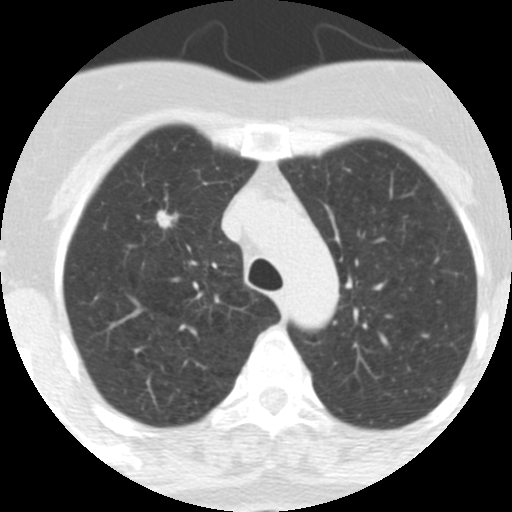
Axial slice from a low-dose chest CT screening exam; baseline annual screen; lung window (W 1500 / L -600 HU); 2.5 mm slice thickness; 120 kVp; slice 74 of 313 in the series. Female participant, aged 62 years at enrolment. Current smoker at enrolment.
Expert-annotated lung lesion, bounding box [x1, y1, x2, y2] px = [116, 161, 182, 233]. The exam's reader record, not a measurement of the box and not confirmed to be the same lesion: non-calcified nodule or mass ≥4 mm, right upper lobe, 9 × 7 mm, spiculated (stellate) margins, soft tissue attenuation. Participant outcome: lung cancer diagnosed 126 days after this screen — adenocarcinoma, NOS, right upper lobe, moderately differentiated (G2), stage IA (AJCC 6th edition), 18 mm at pathology.